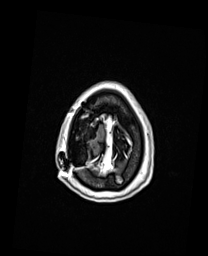
Brain MRI from a brain-tumour surgery series, one axial slice; position 26 of 192 along the scan axis; T1-weighted post-contrast; 1 mm slice thickness; 208 × 256 image matrix. Case-level facts recorded for this patient, not image findings: histopathology: Oligodendroglioma; WHO grade: 3; IDH mutation: yes; tumour location: Right Frontal.
Annotated regions visible in this slice (manually delineated by an expert):
- previous resection cavity: bounding box [x1, y1, x2, y2] px = [85, 129, 96, 141]